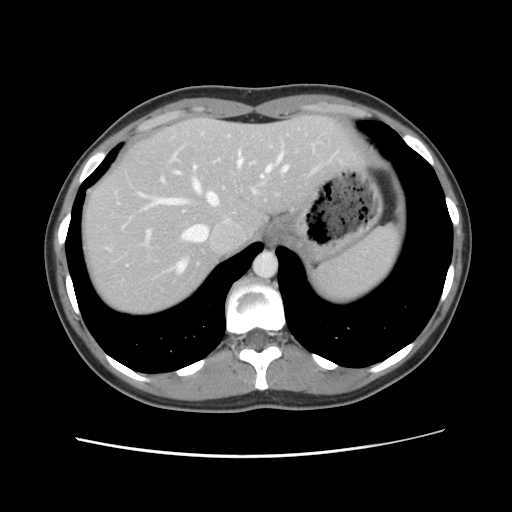
Contrast-enhanced abdominal CT, one axial slice; position 96 of 134 along the scan axis; intravenous contrast given; soft-tissue window (W 400 / L 40 HU); 512 × 512 image matrix, field of view 339 × 339 mm. Female patient, age 33 years. Case-level facts recorded for this patient, not image findings: diagnosis: colorectal cancer liver metastases, imaged before liver resection; multiple liver metastases: yes; largest metastasis: 4.5 cm; disease in both lobes: yes.
Outlined on this slice (manually delineated by an expert):
- hepatic veins: box from (x=140, y=151) to (x=289, y=273) px
- liver: (x=81, y=116)–(x=361, y=316)
- planned liver remnant (the part of the liver to remain after resection): (x=81, y=116)–(x=362, y=316)
- portal vein (with intrahepatic branches): (x=117, y=201)–(x=153, y=248)